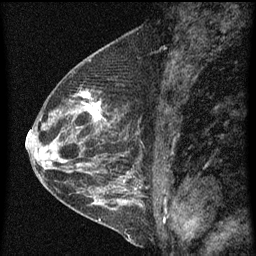
Breast MRI (dynamic contrast-enhanced), one sagittal slice. Position 26 of 60 along the scan axis. Dynamic contrast-enhanced series, image 2 of 4 at this slice position (ordered by acquisition). 1.5 T. TE 4.2 ms, TR 8 ms. 2 mm slice thickness. 256 × 256 image matrix, field of view 180 × 180 mm. Patient: female, 48 years.
Structures marked on this image (semi-automatic segmentation, software-assisted and operator-edited):
- analysis volume of interest (the breast-tissue region the enhancement analysis was run in; not a lesion): bounding box <73,84,115,139> (left, top, right, bottom; pixels)
- tumour enhancement mask (voxels above the 70 % enhancement threshold inside the analysis volume of interest): <81,90,106,123>